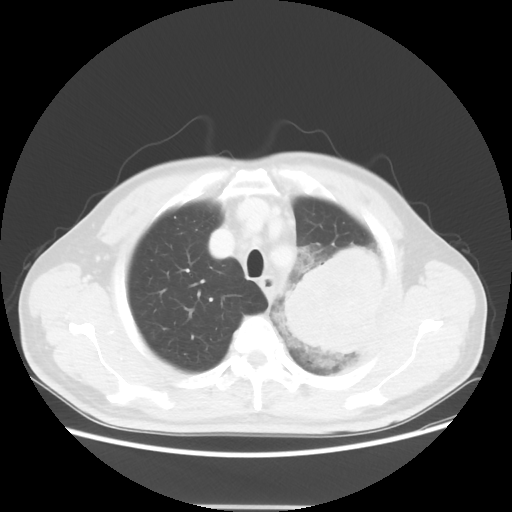
Chest CT, one axial slice; position 45 of 53 along the scan axis; reconstruction kernel STANDARD; 100 kVp; lung window (W 1500 / L -600 HU); 5 mm slice thickness; 512 × 512 image matrix, field of view 391 × 391 mm. Male patient, age 60 years. From the clinical record (not read from this slice): clinical TNM (as recorded): T4 N1 M1a.
Structures marked on this image (rectangle marked by the reading radiologist):
- lung tumour (recorded histology: large cell carcinoma): box from (x=269, y=236) to (x=383, y=363) px